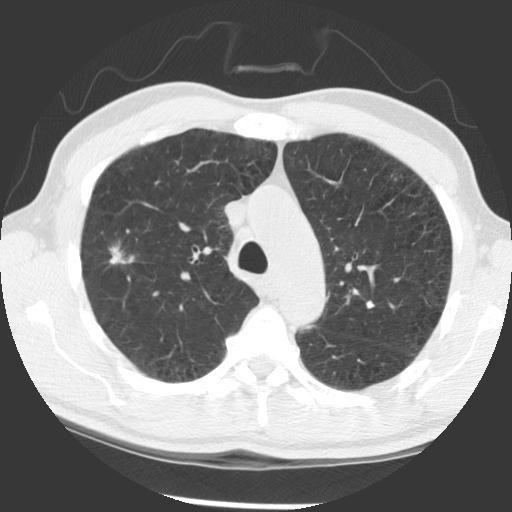
Low-dose screening chest CT, axial slice, baseline annual screen, lung window (W 1500 / L -600 HU), 2.5 mm slice thickness, standard (soft-tissue) reconstruction kernel (STANDARD), slice 100 of 140 in the series. Male, age 56 years at enrolment. Current smoker at enrolment.
Expert-annotated lung lesion, bounding box (x1, y1, x2, y2) in pixels: (72, 230, 142, 287). The exam's reader record, not a measurement of the box and not confirmed to be the same lesion: non-calcified nodule or mass ≥4 mm, right upper lobe, 12 × 7 mm, spiculated (stellate) margins, soft tissue attenuation. Official screen result: positive, change unspecified: nodule(s) >= 4 mm or enlarging nodule(s), mass(es), or other non-specific abnormalities suspicious for lung cancer. Participant outcome: lung cancer diagnosed 676 days after this screen (after the second annual screen) — squamous cell carcinoma, NOS, right upper lobe, right middle lobe, moderately differentiated (G2), stage IB (AJCC 6th edition), 70 mm at pathology.